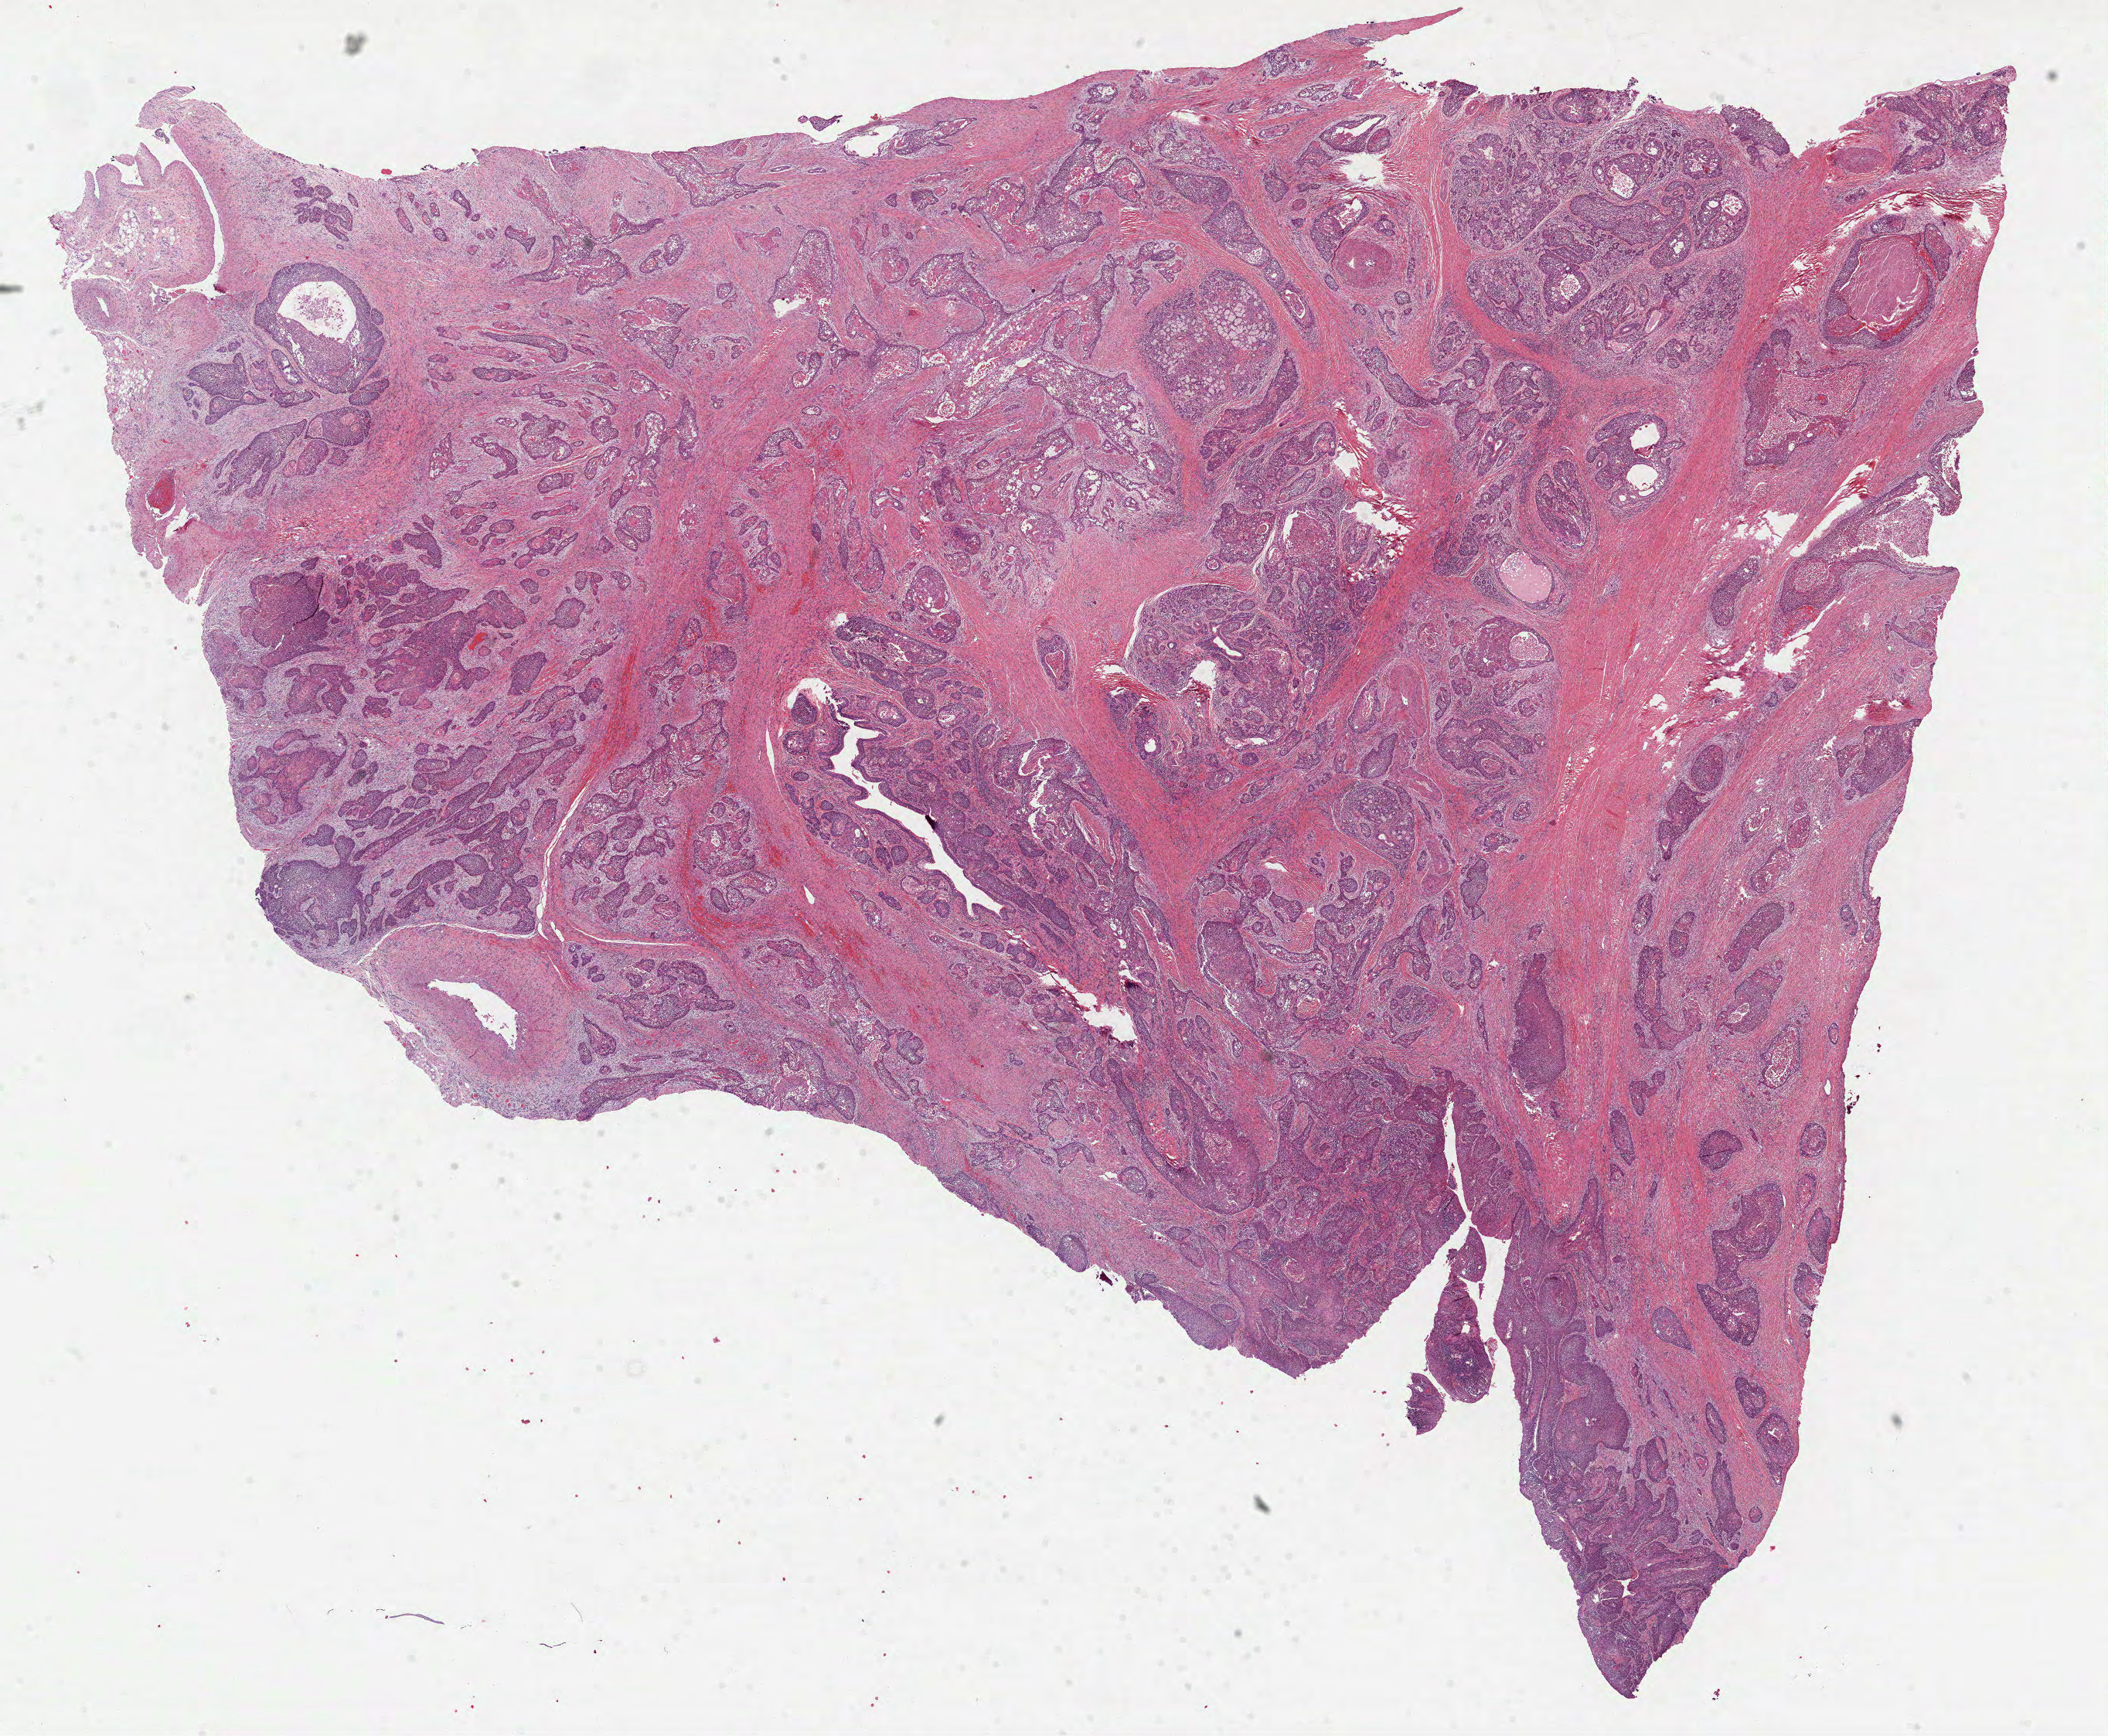
H&E-stained whole-slide image — whole scanned area (about 22.0 x 18.1 mm, from a 40x scan) shown as a low-resolution overview. FFPE section. Primary tumour sample from the head and neck. Patient: male, age at initial diagnosis 55 years. Histologic grade: G2 (moderately differentiated).
• AJCC pathologic stage: IVA (6th edition)
• pathologic diagnosis: Squamous cell carcinoma, NOS (floor of mouth, NOS)
• TNM: T4a N2c M0